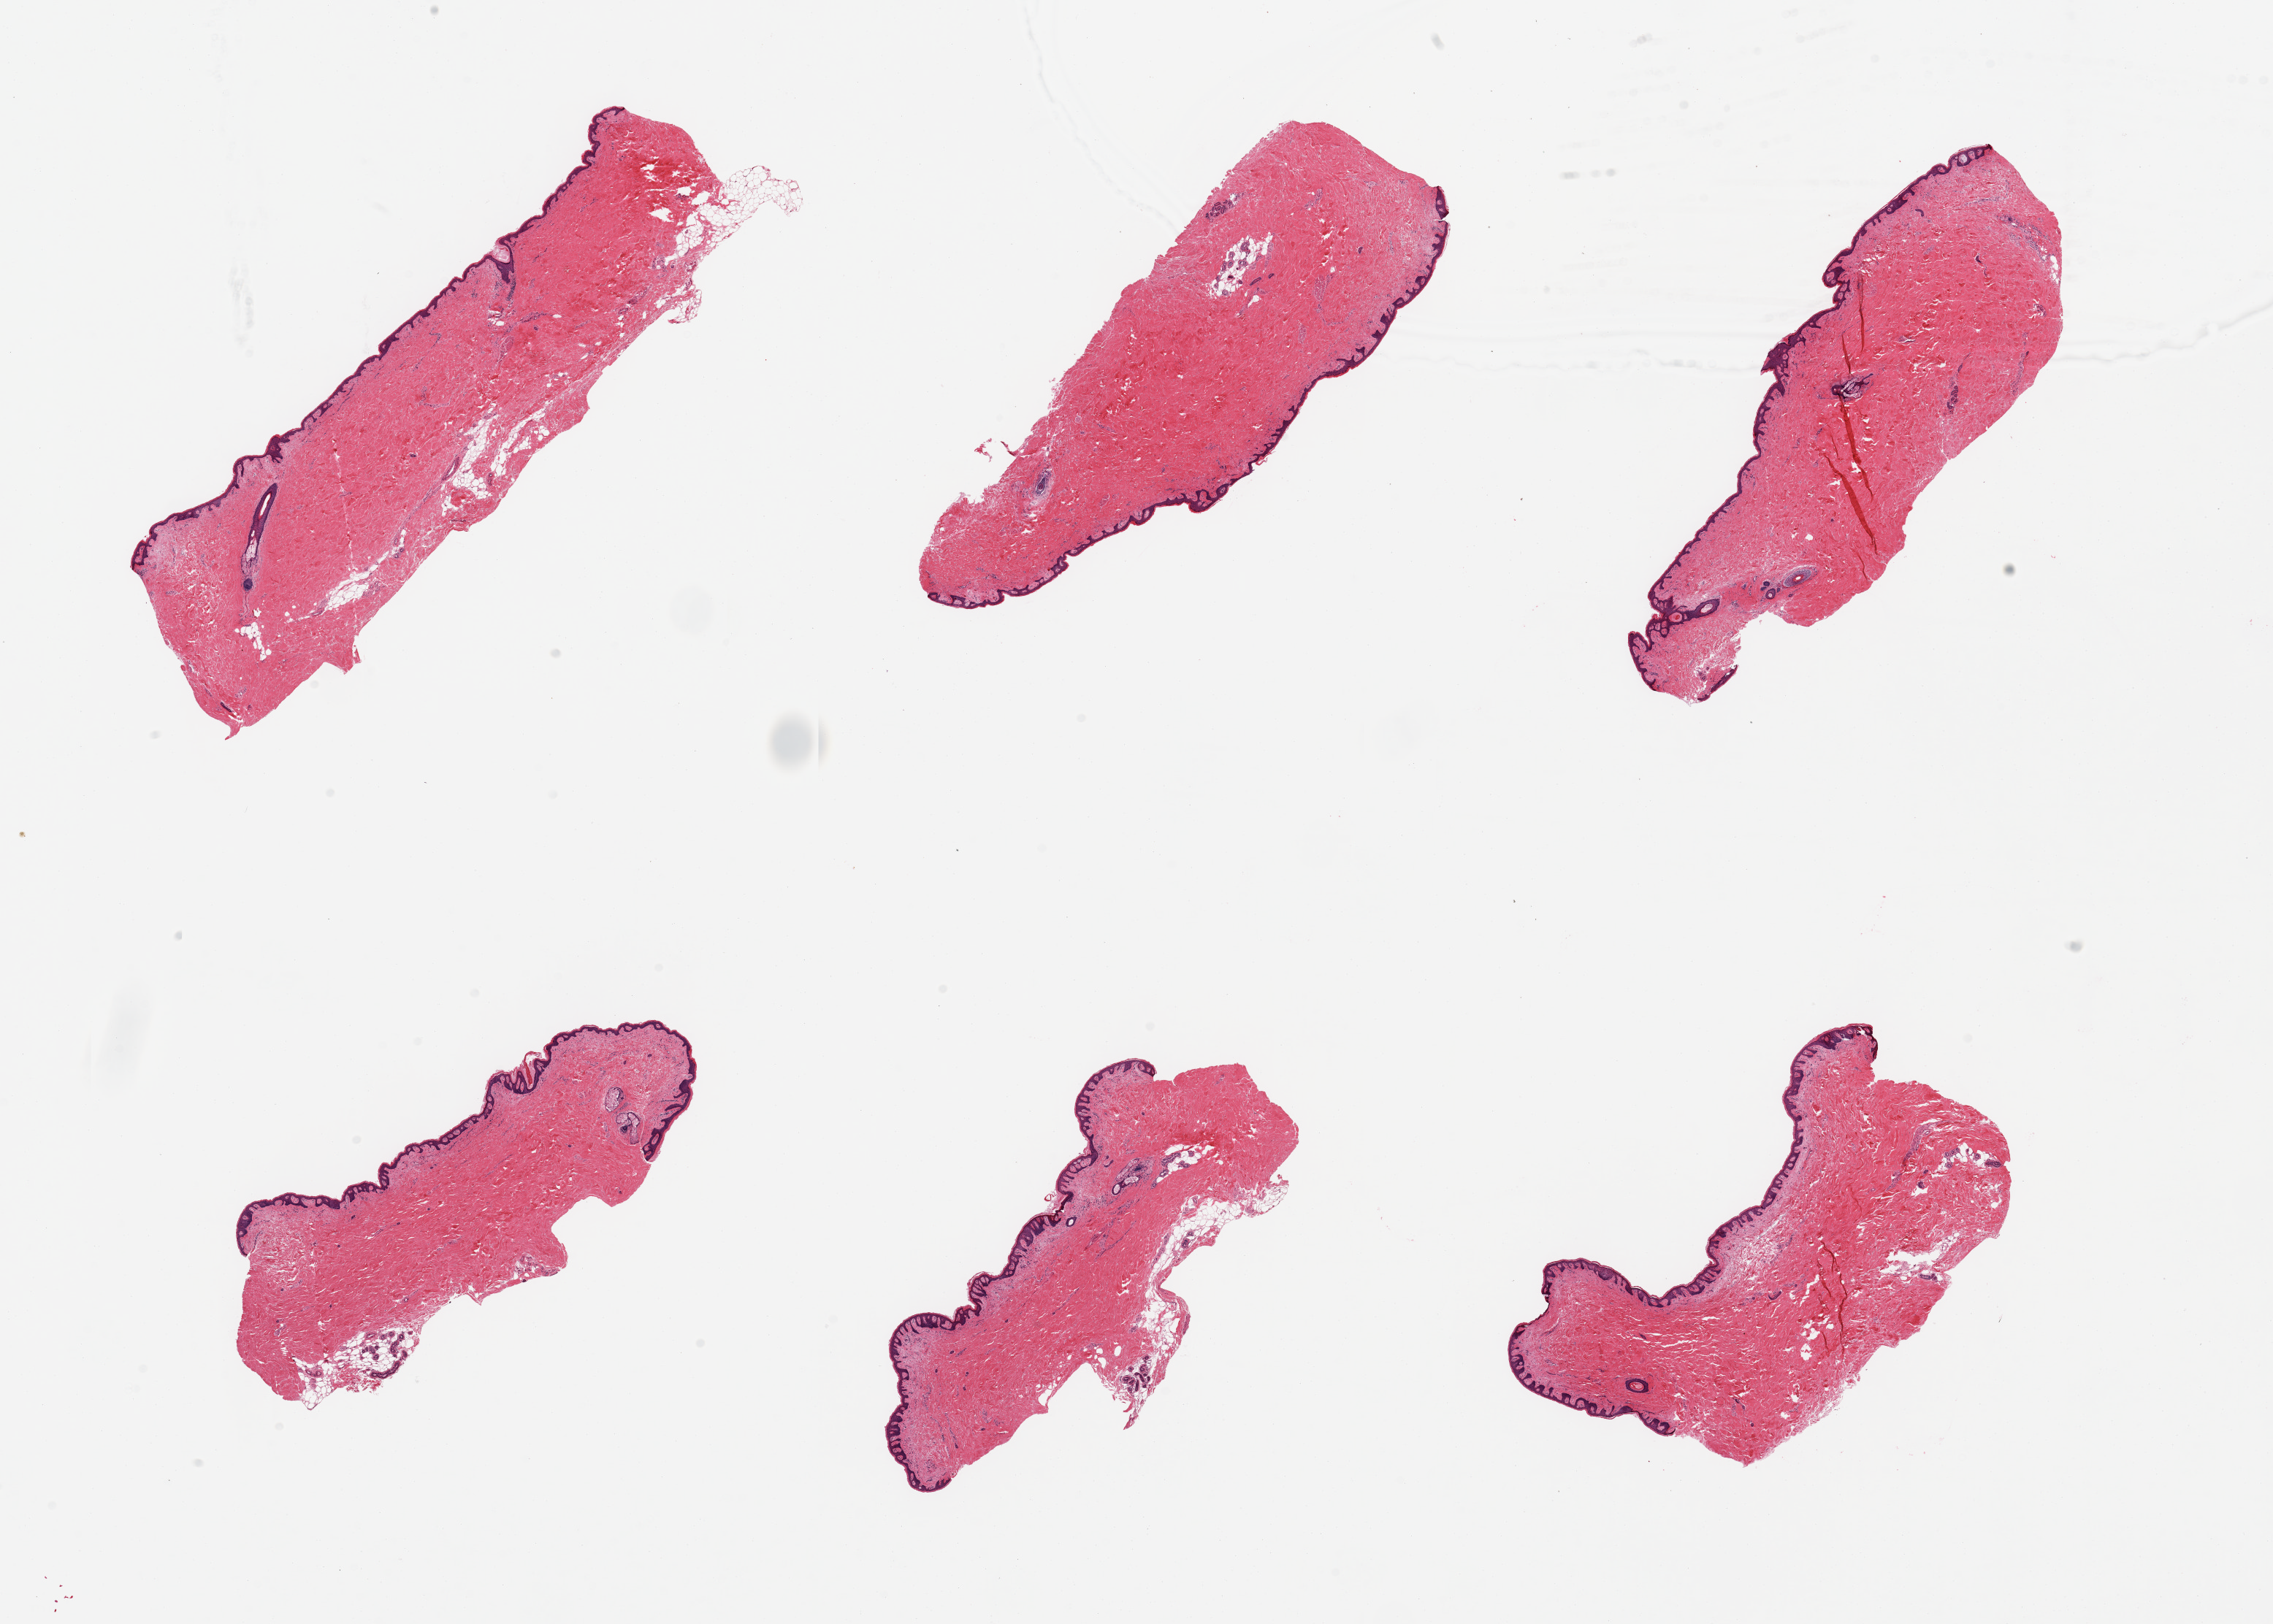
H&E whole-slide image, a low-resolution overview of the entire scanned area, about 24.6 x 17.6 mm (from a 20x scan). PAXgene-fixed, paraffin-embedded tissue. Target tissue: skin of suprapubic region. Donor tissue sample. Male donor.
Reviewer comment on this tissue sample: 6 pieces, minimal dermal fat, sqauamous epithelium is ~ microns.